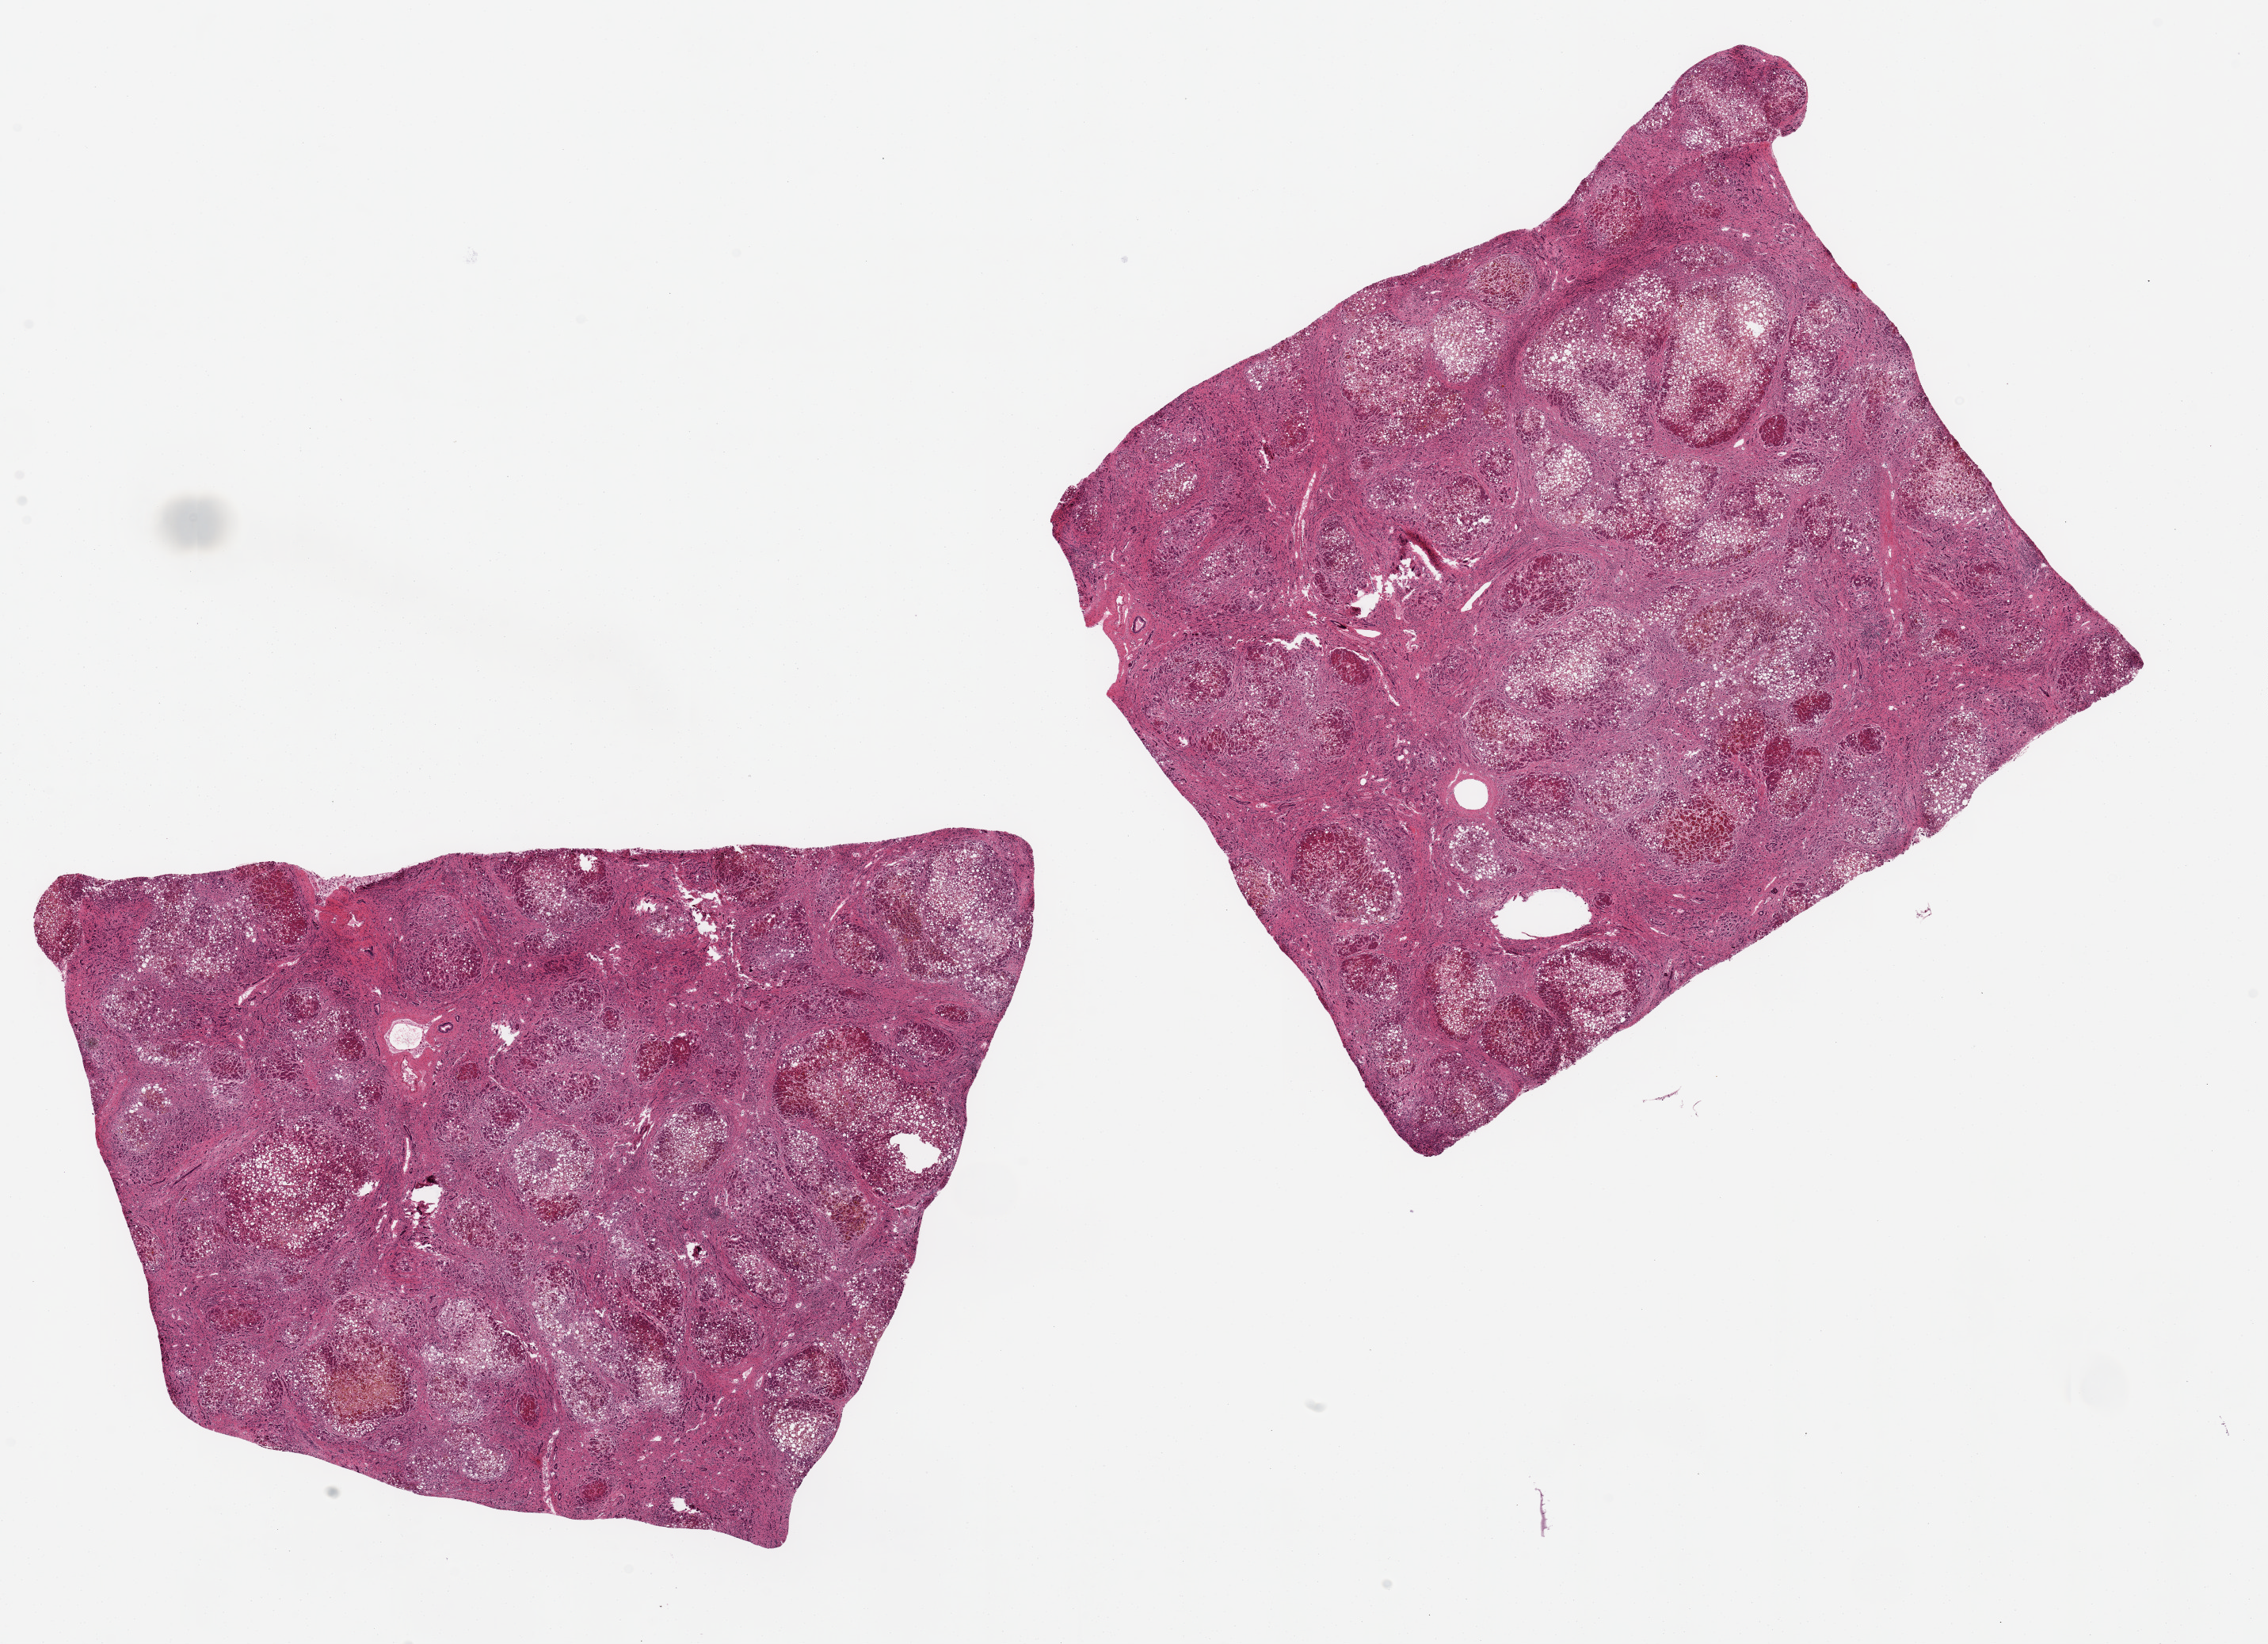
Whole-slide image, hematoxylin and eosin (H&E) stain, whole scanned area (about 22.6 x 16.4 mm) shown as a low-resolution overview, PAXgene-fixed paraffin-embedded (PFPE) section, sampled site (target tissue): liver, donor tissue sample. Donor sex: female.
- reviewer comment on this tissue sample: 2 ~9x7mm aliquots. Established cirrhosis with steatohepatitis, diffuse